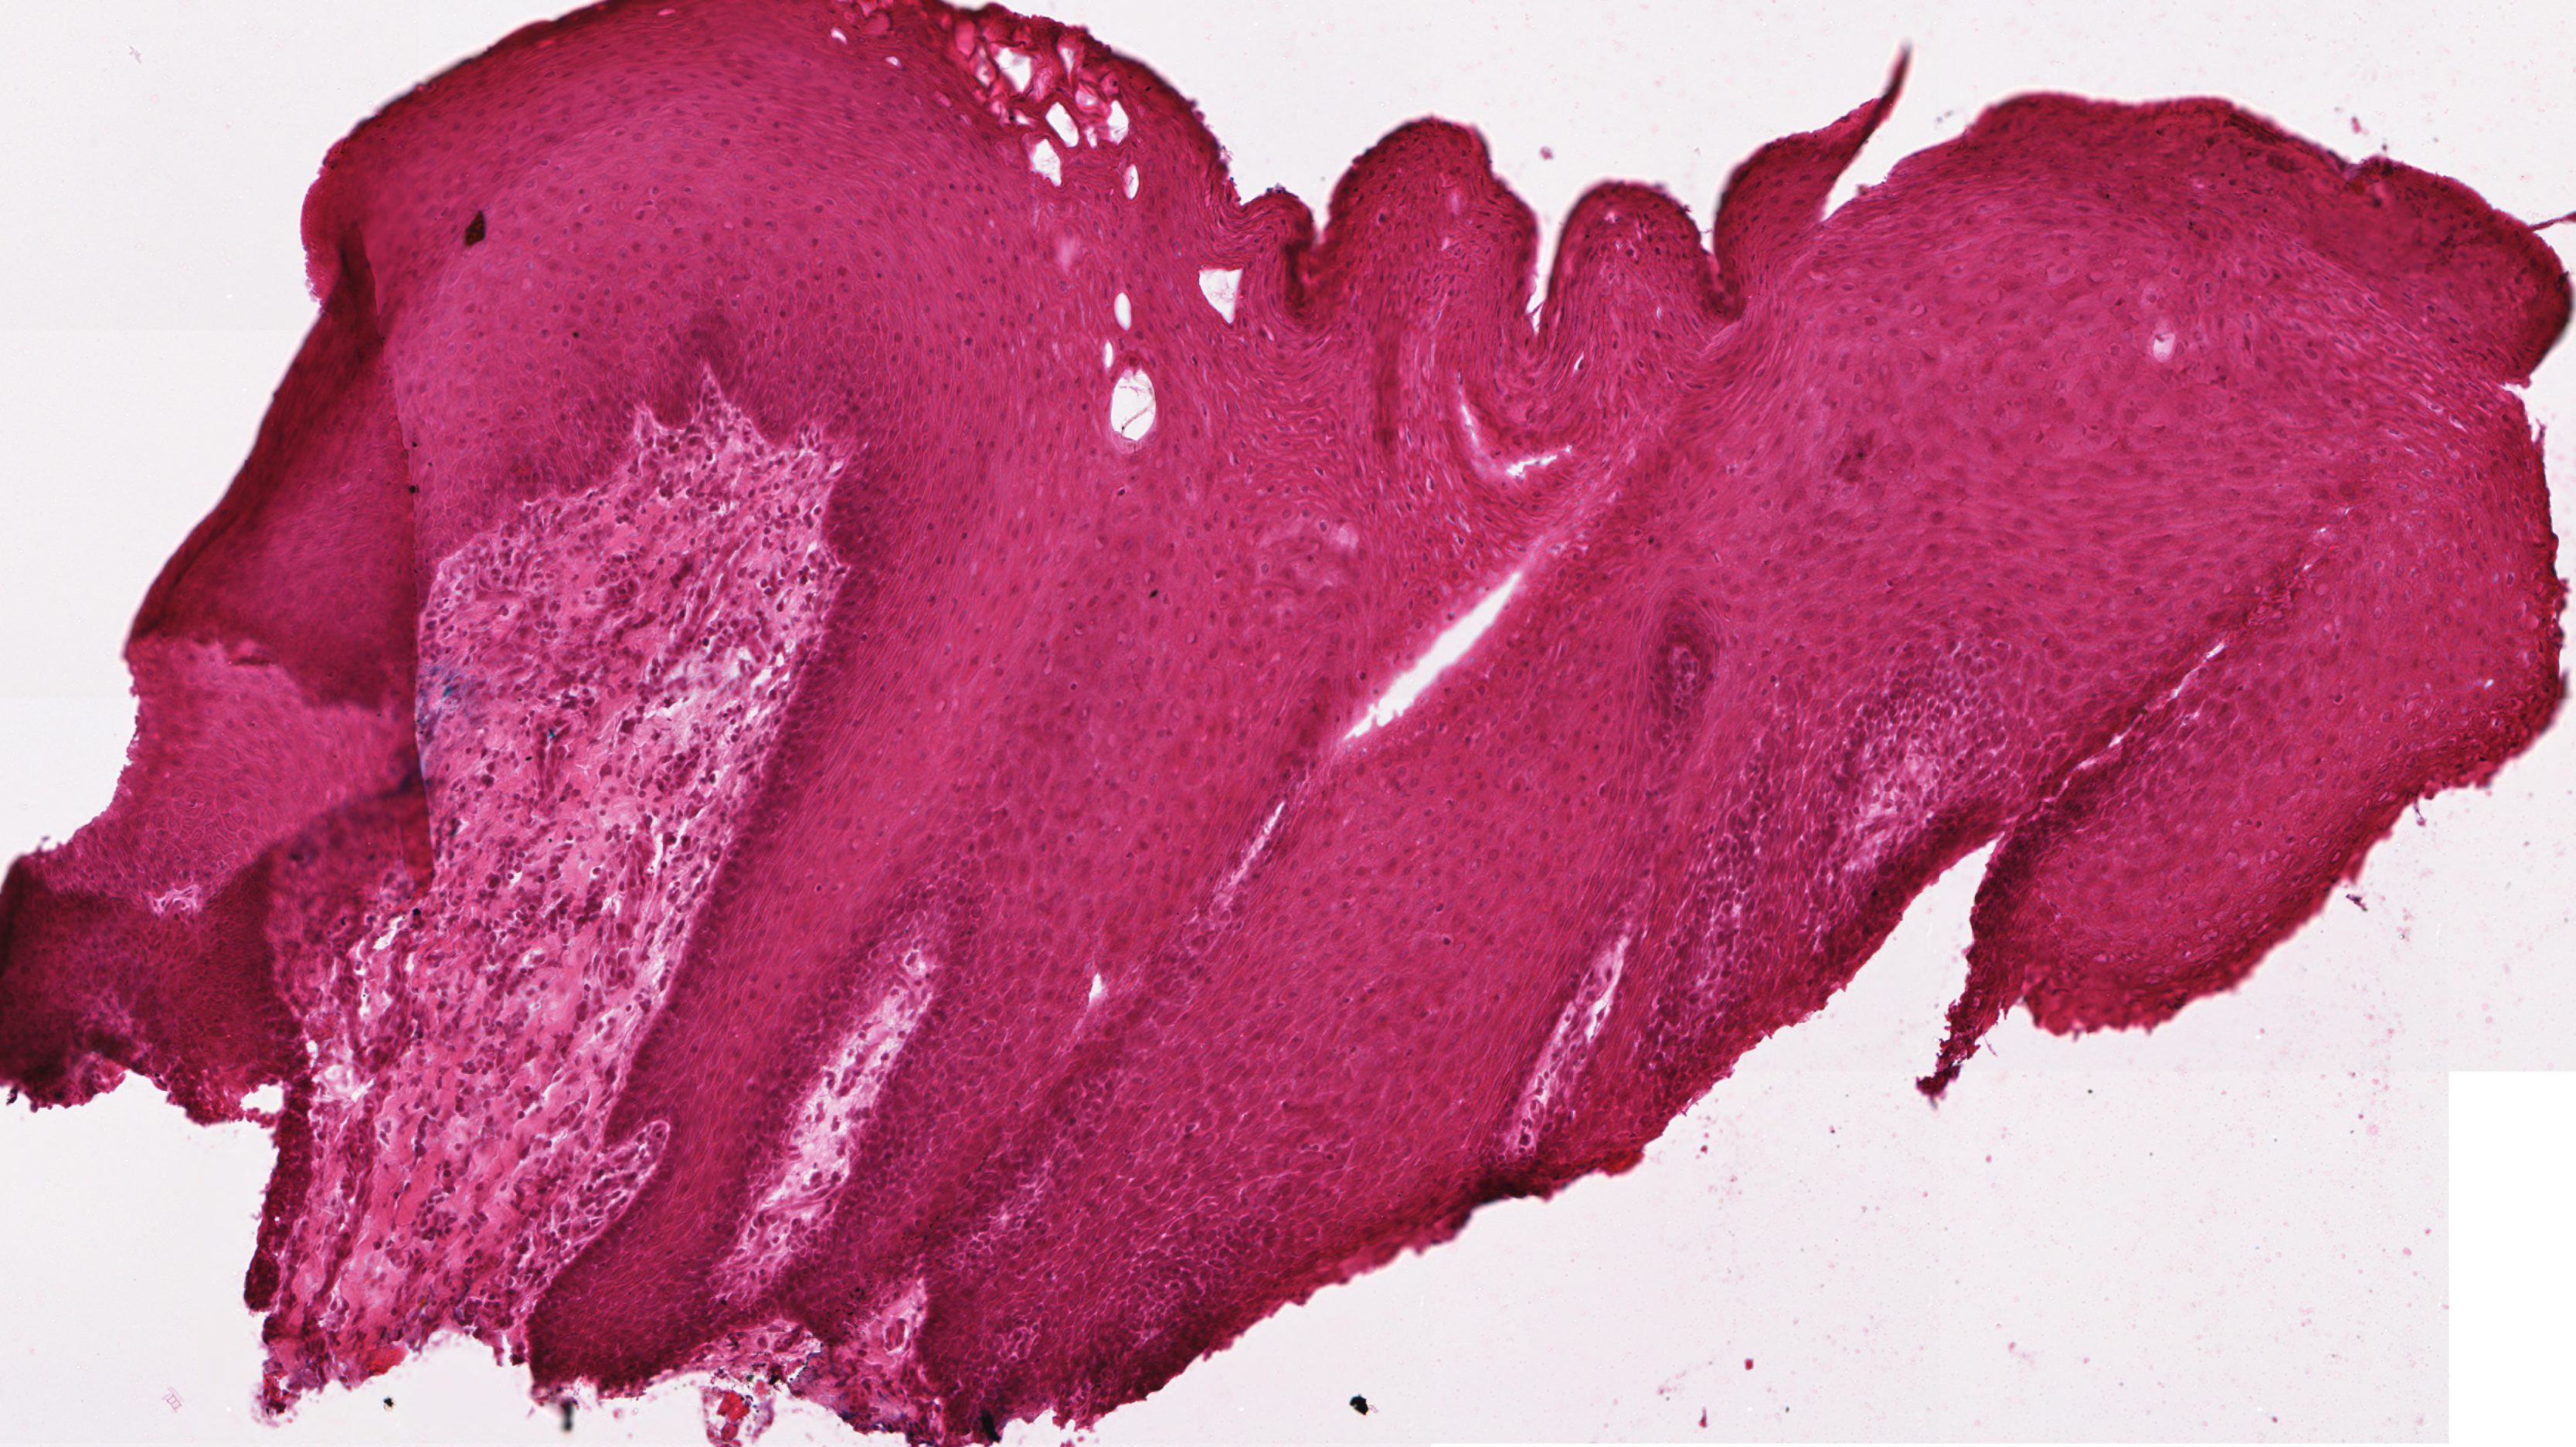
Whole-slide histology image, H&E, whole scanned area (about 3.3 x 1.9 mm) shown as a low-resolution overview, frozen section from the top of the tissue portion, sample: primary tumour, head and neck. Patient: female, age at initial diagnosis 36 years. Histologic grade: G1 (well differentiated). Composition of this section per pathologist review: tumour cells 85%, tumour nuclei 80%, normal cells 0%, stromal cells 15%, necrosis 0%. Inflammatory infiltration, as recorded: lymphocyte infiltration 16%, monocyte infiltration 0%, neutrophil infiltration 0%.
AJCC pathologic stage: I (6th edition). Pathologic diagnosis: Squamous cell carcinoma, NOS. Laterality: left.